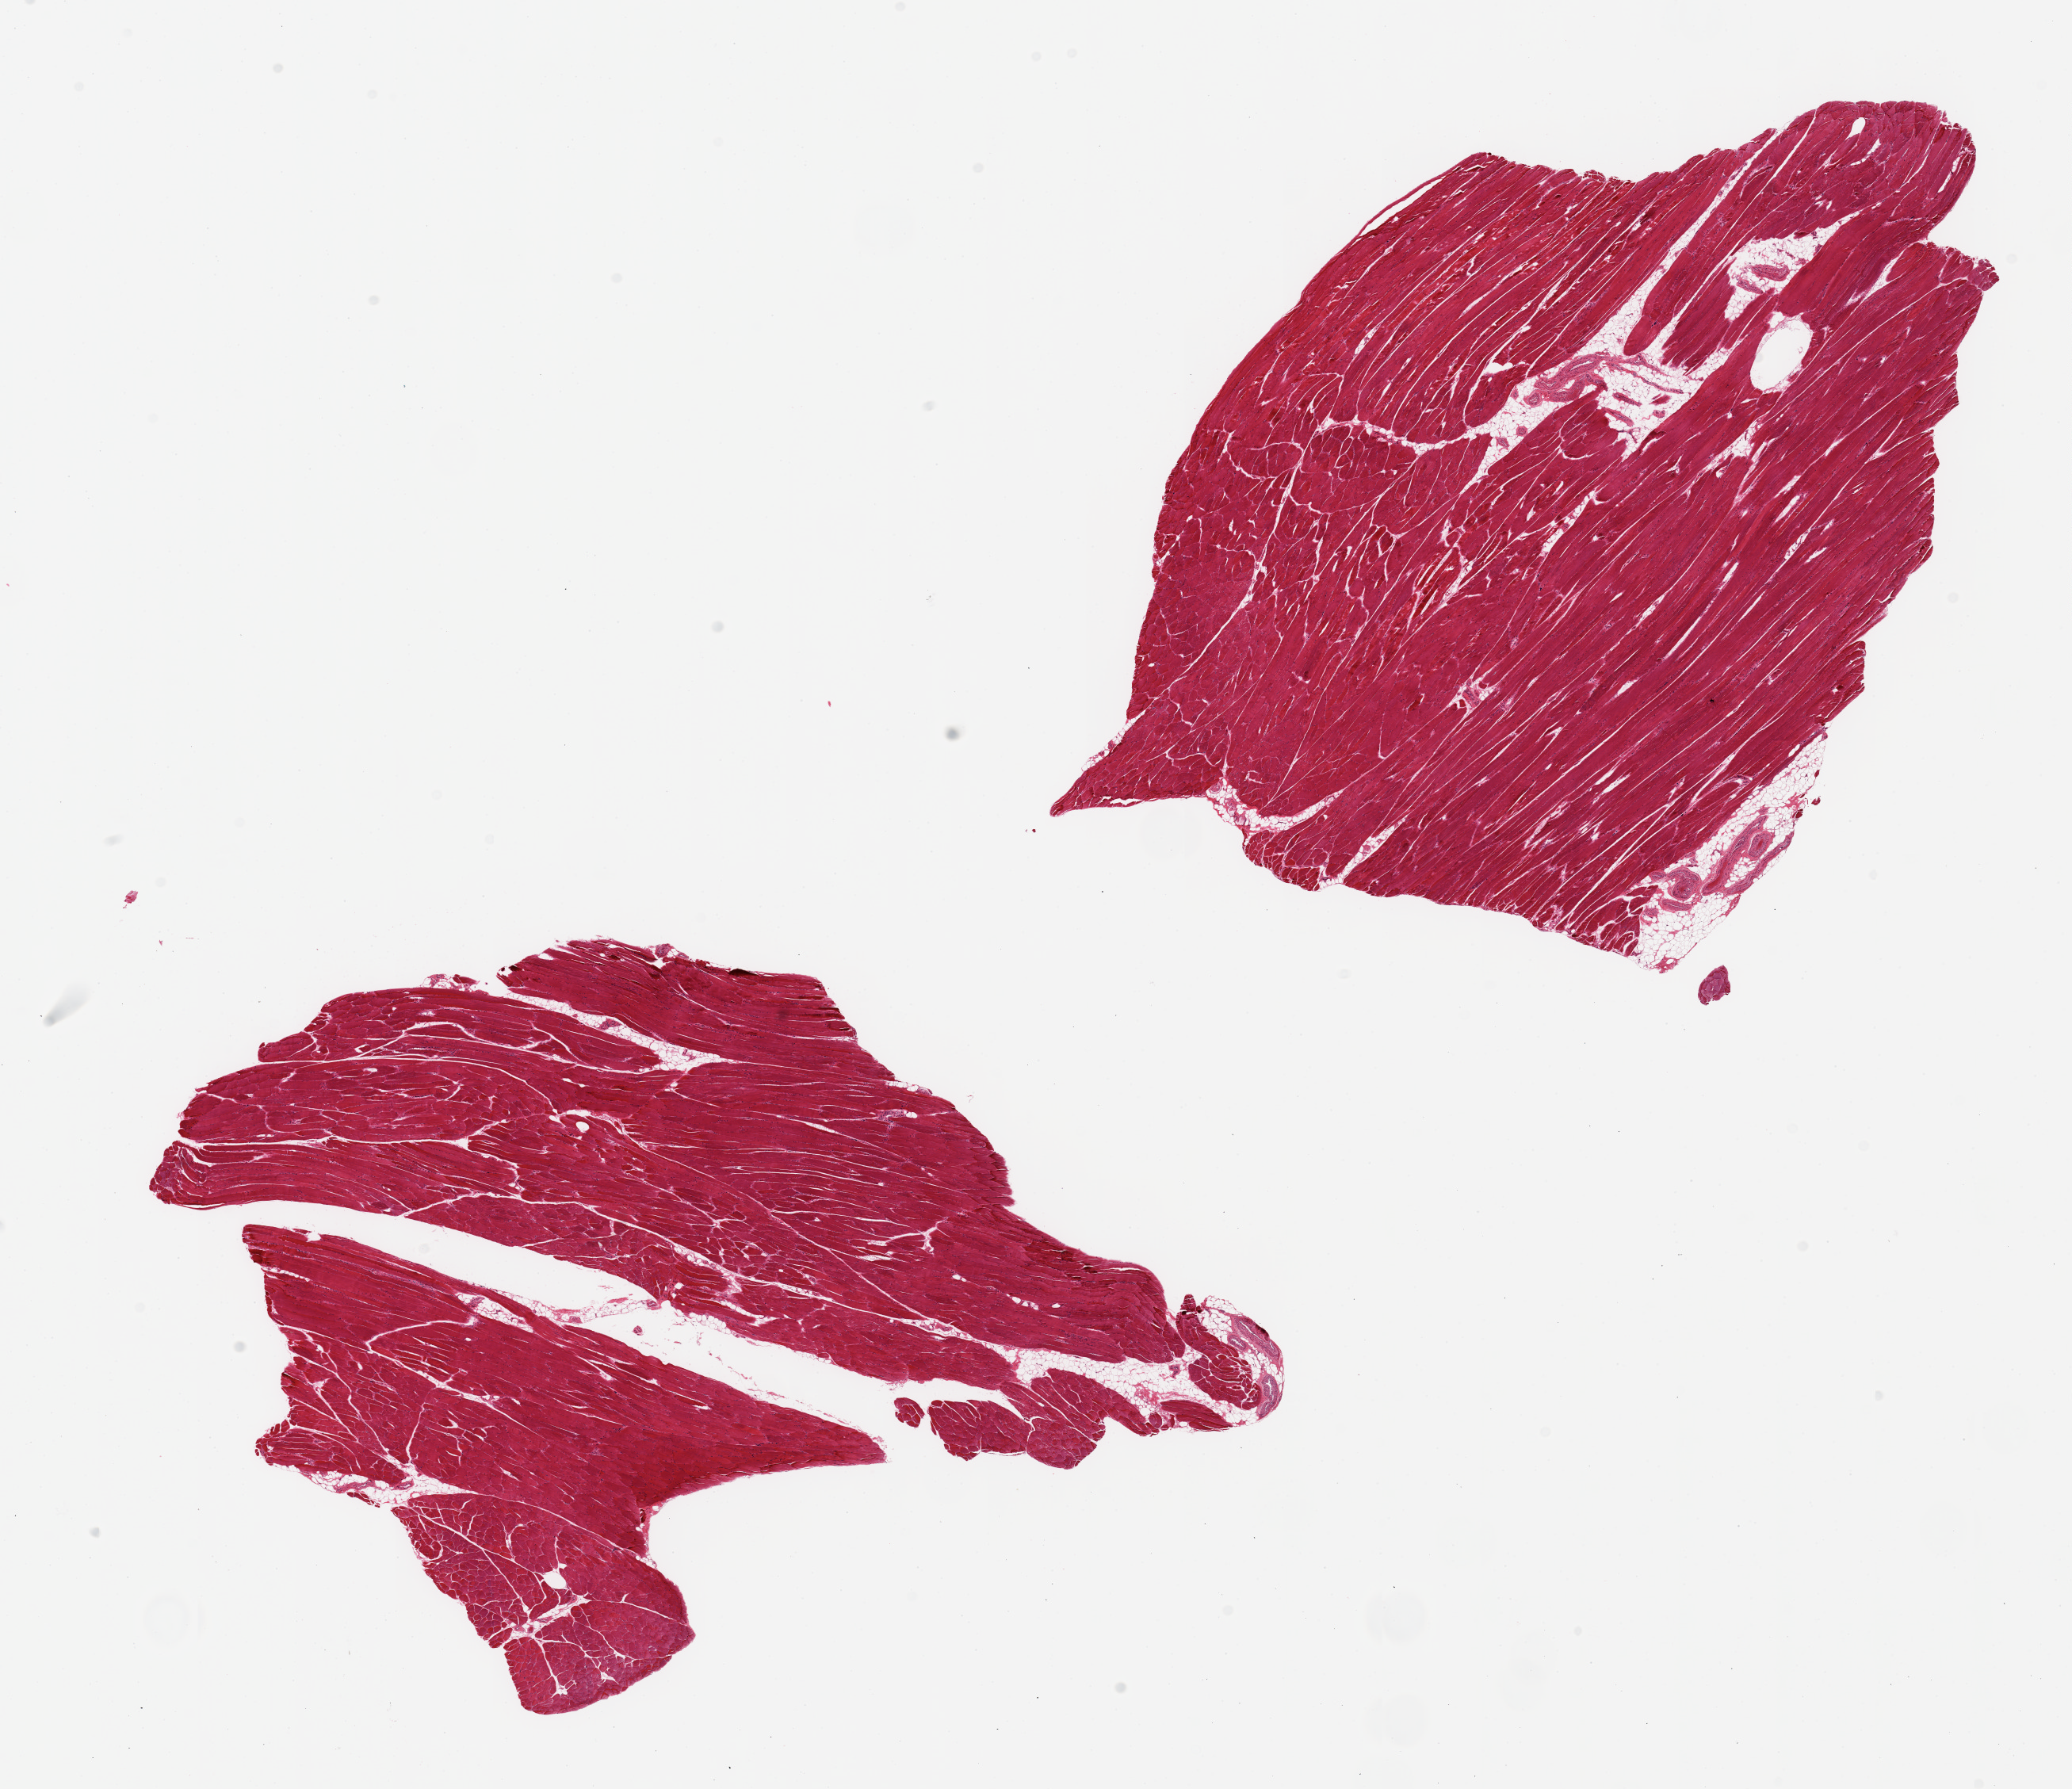
Whole-slide image, H&E stain, a low-resolution overview of the entire scanned area, about 20.7 x 17.8 mm (slide scanned at 20x). PAXgene-fixed, paraffin-embedded tissue. Sampled site (target tissue): skeletal muscle. Tissue donor sample. Donor: female.
Pathologist's review note for this sample: 2 pieces; 10% internal fat.